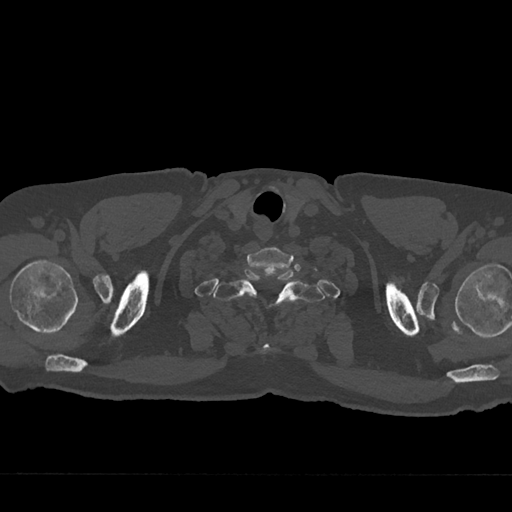
CT including the spine, one axial slice; slice 670 of 797 in the series (ordered by position); reconstruction kernel Br40s/3; 120 kVp; bone window (W 1800 / L 400 HU); 512 × 512 image matrix, field of view 377 × 377 mm. Patient: male, 75 years. From the clinical record (not read from this slice): primary cancer: renal.
Structures marked on this image (semi-automatically segmented with operator editing):
- T1 vertebra: bounding box (x1, y1, x2, y2) in pixels: (213, 269, 324, 353)